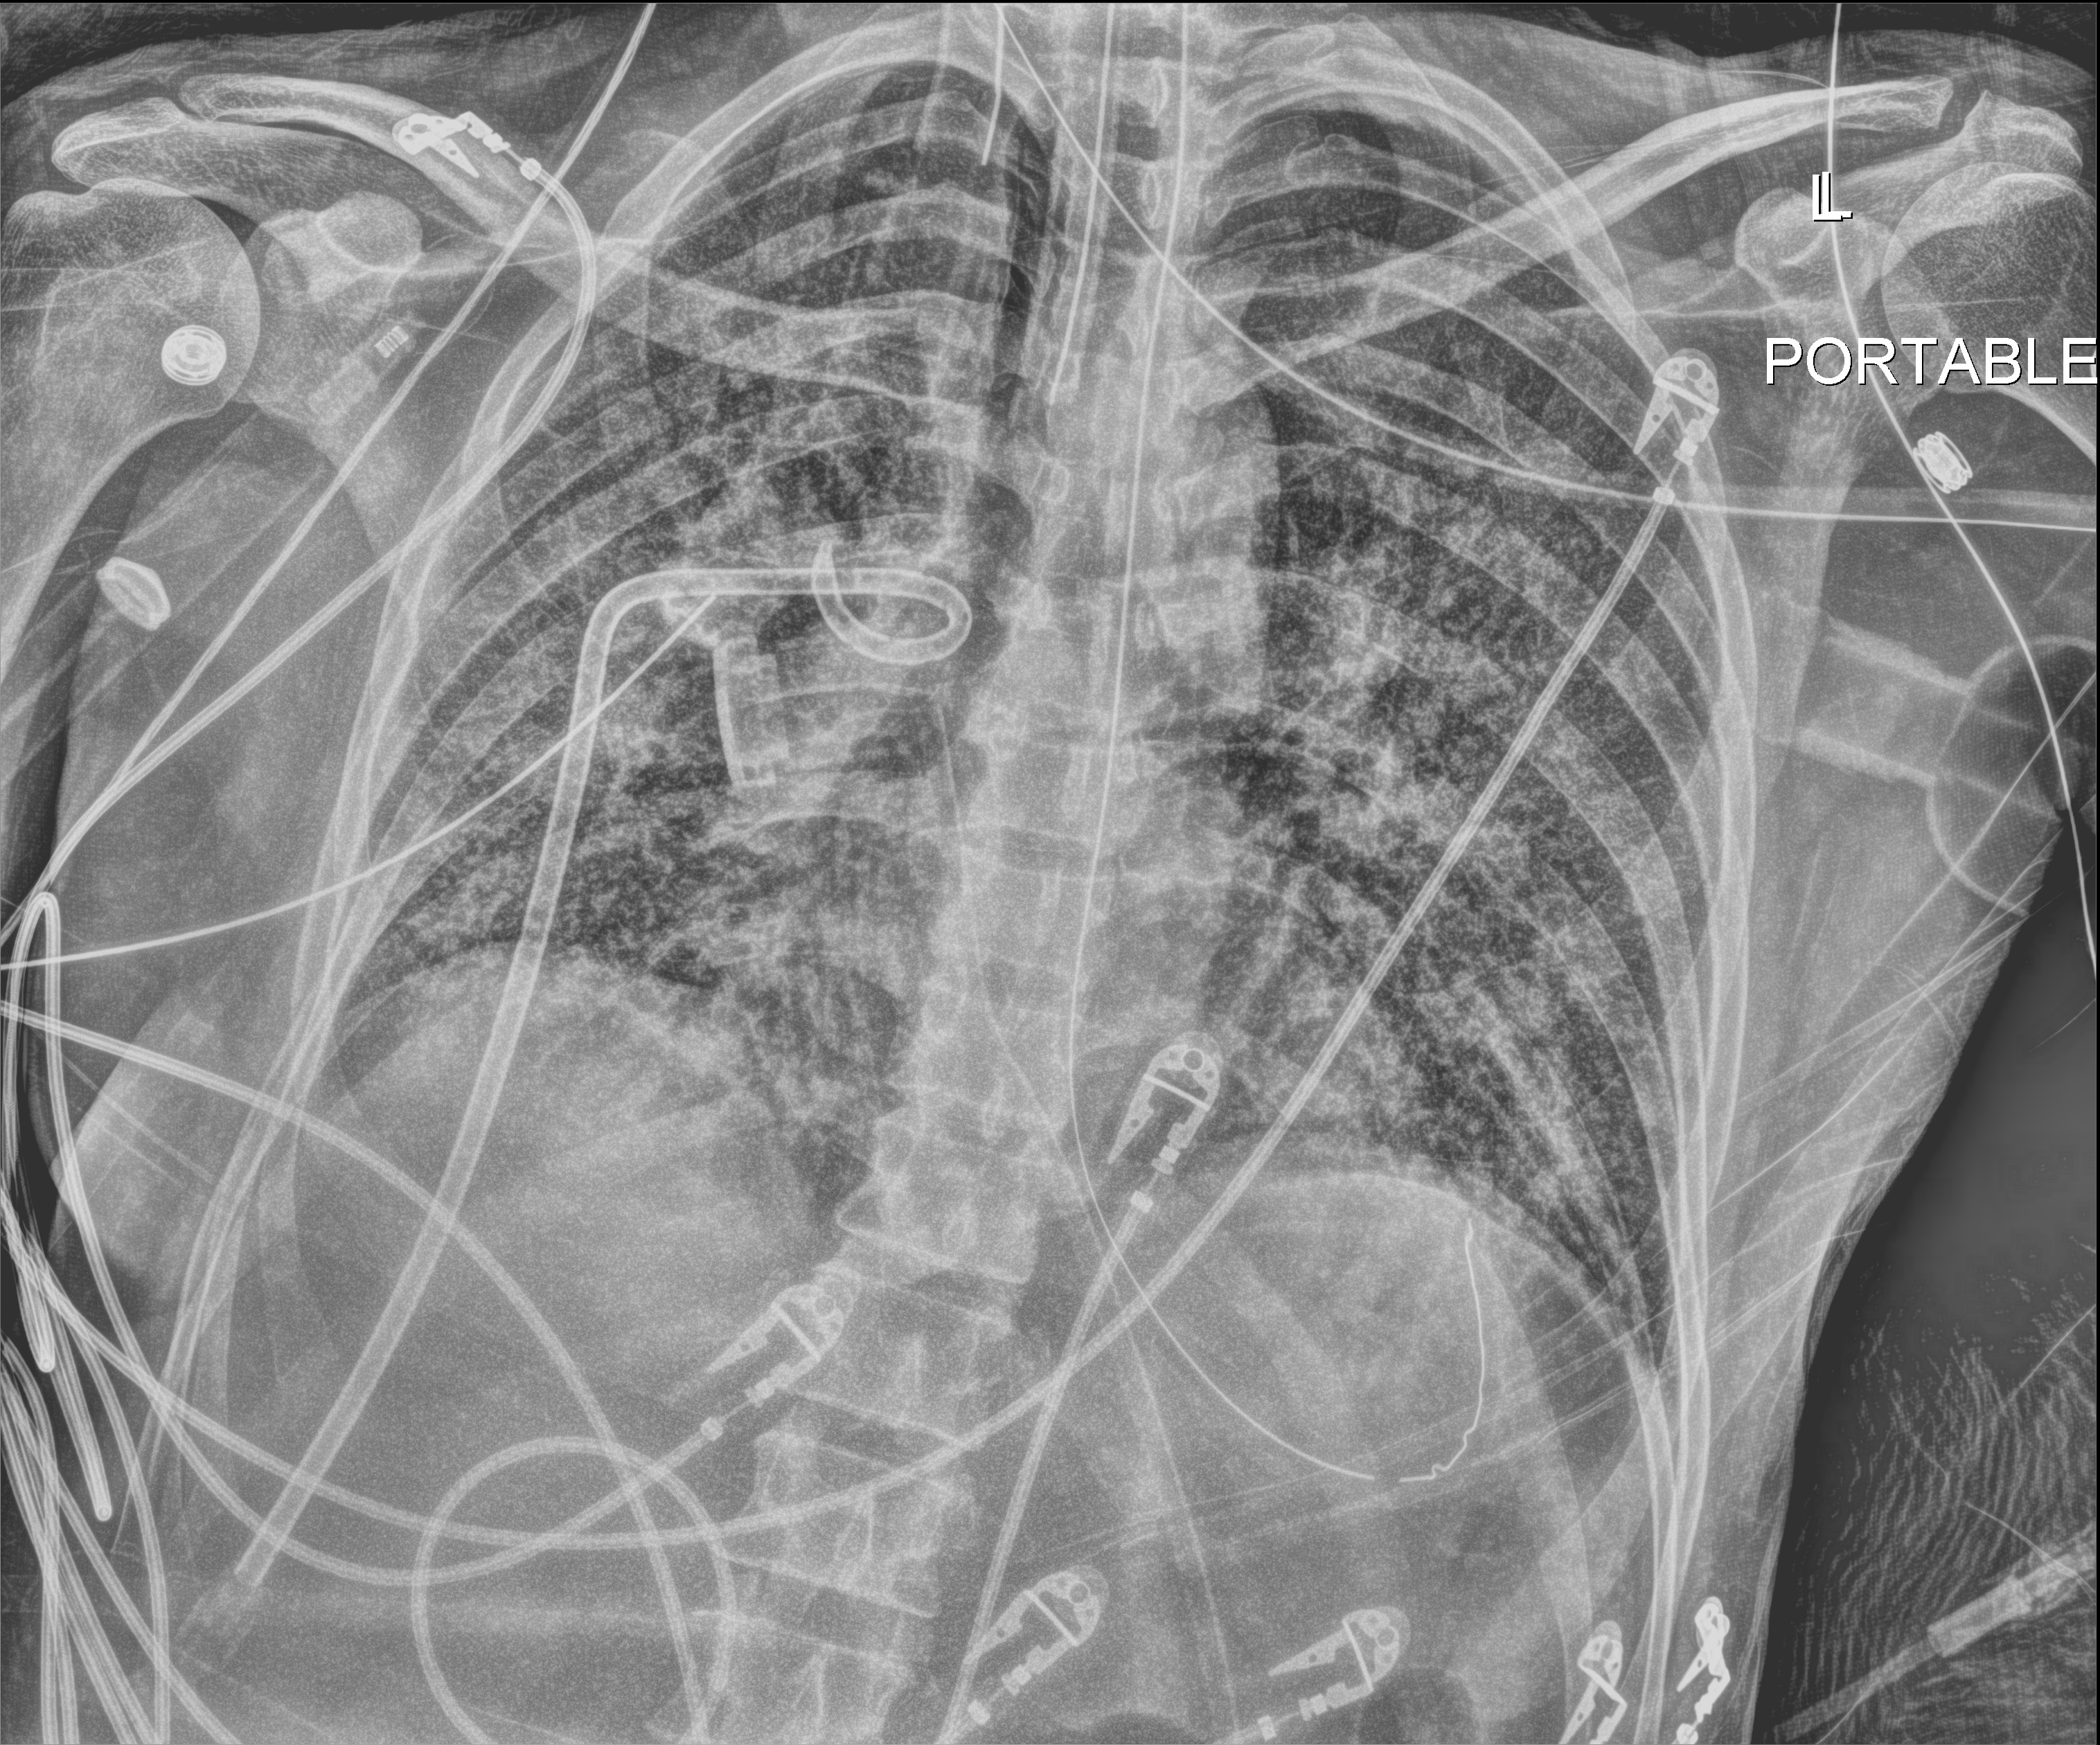
Chest radiograph (digital radiography). Adult patient hospitalised with COVID-19, age 18–59 years.
From the hospital-stay record, not from the radiograph (when in the stay this image was taken is not recorded):
- admitted to intensive care during this hospital stay: yes